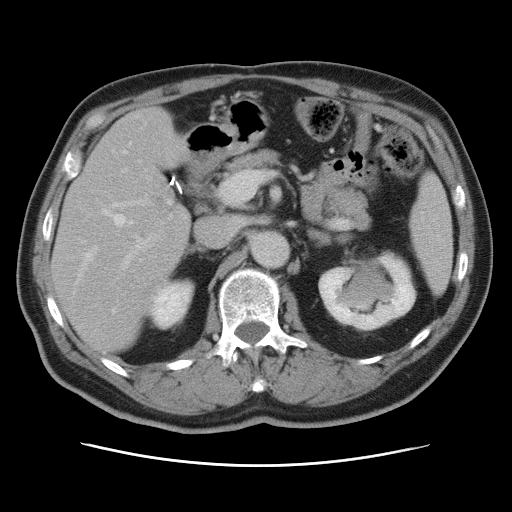
Contrast-enhanced abdominal CT, one axial slice; position 42 of 80 along the scan axis; 120 kVp; intravenous contrast given; soft-tissue window (W 400 / L 40 HU); 5 mm slice thickness; 512 × 512 image matrix, field of view 370 × 370 mm. Male patient, age 69 years. From the clinical record (not read from this slice): diagnosis: colorectal cancer liver metastases, imaged before liver resection; multiple liver metastases: no.
Outlined on this slice (expert manual segmentation):
- hepatic veins: bounding box (x1, y1, x2, y2) in pixels: (78, 152, 132, 313)
- liver: (54, 110, 188, 352)
- planned liver remnant (the part of the liver to remain after resection): (54, 187, 189, 352)
- portal vein (with intrahepatic branches): (121, 170, 171, 270)